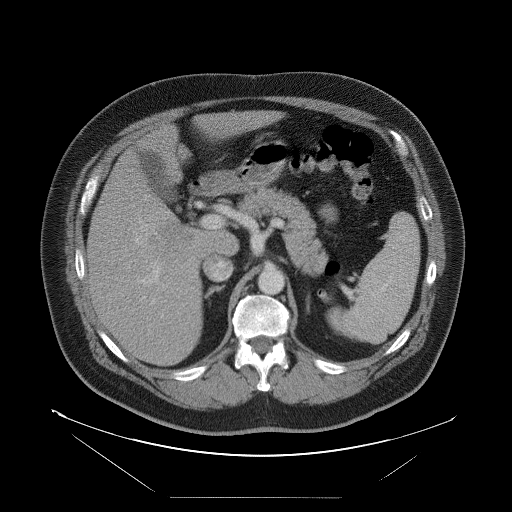
Contrast-enhanced abdominal CT, one axial slice. Position 56 of 114 along the scan axis. 120 kVp. Soft-tissue window (W 400 / L 40 HU). 5 mm slice thickness. 512 × 512 image matrix, field of view 500 × 500 mm. Male patient, age 61 years. Case-level facts recorded for this patient, not image findings: diagnosis: colorectal cancer liver metastases, imaged before liver resection; multiple liver metastases: no; largest metastasis: 6.5 cm; disease in both lobes: yes.
Structures marked on this image (expert manual segmentation):
- liver: bounding box [x1, y1, x2, y2] px = [89, 112, 274, 366]
- planned liver remnant (the part of the liver to remain after resection): [146, 112, 275, 177]
- portal vein (with intrahepatic branches): [141, 217, 210, 301]
- liver metastasis: [152, 224, 190, 251]